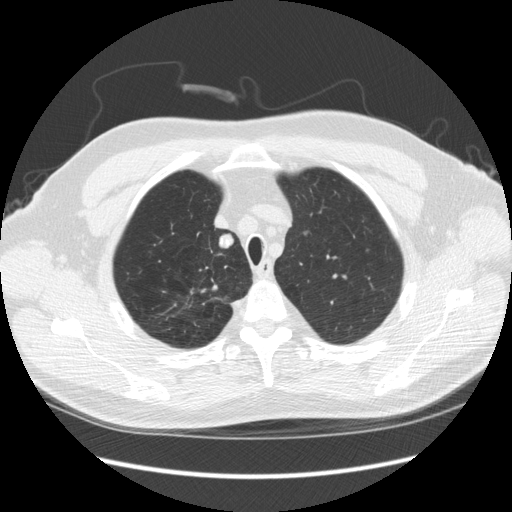
Low-dose screening chest CT, axial slice, third annual screen, lung window (W 1500 / L -600 HU), standard (soft-tissue) reconstruction kernel (STANDARD), slice 37 of 248 in the series. Male, age 64 years at enrolment. Former smoker at enrolment.
Expert-annotated lung lesion, bounding box (x1, y1, x2, y2) in pixels: (200, 230, 242, 260). The screening reader recorded 4 non-calcified nodules or masses ≥4 mm on this exam; which of them this box marks is not recorded.